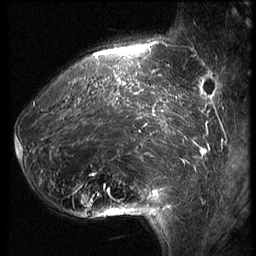
Breast MRI (dynamic contrast-enhanced), one sagittal slice. Position 17 of 62 along the scan axis. 3 images stored at this slice position (order not interpretable as contrast timing). 1.5 T. TE 4.2 ms, TR 9 ms. 256 × 256 image matrix. Patient: female, 39 years. Case-level facts recorded for this patient, not image findings: setting: breast cancer imaged before/during neoadjuvant chemotherapy; receptor status: HER2-positive.
Annotated regions visible in this slice (semi-automatic segmentation, software-assisted and operator-edited):
- analysis volume of interest (the breast-tissue region the enhancement analysis was run in; not a lesion): box from (x=16, y=64) to (x=171, y=228) px
- tumour enhancement mask (voxels above the 140 % enhancement threshold inside the analysis volume of interest): (x=16, y=73)–(x=171, y=213)